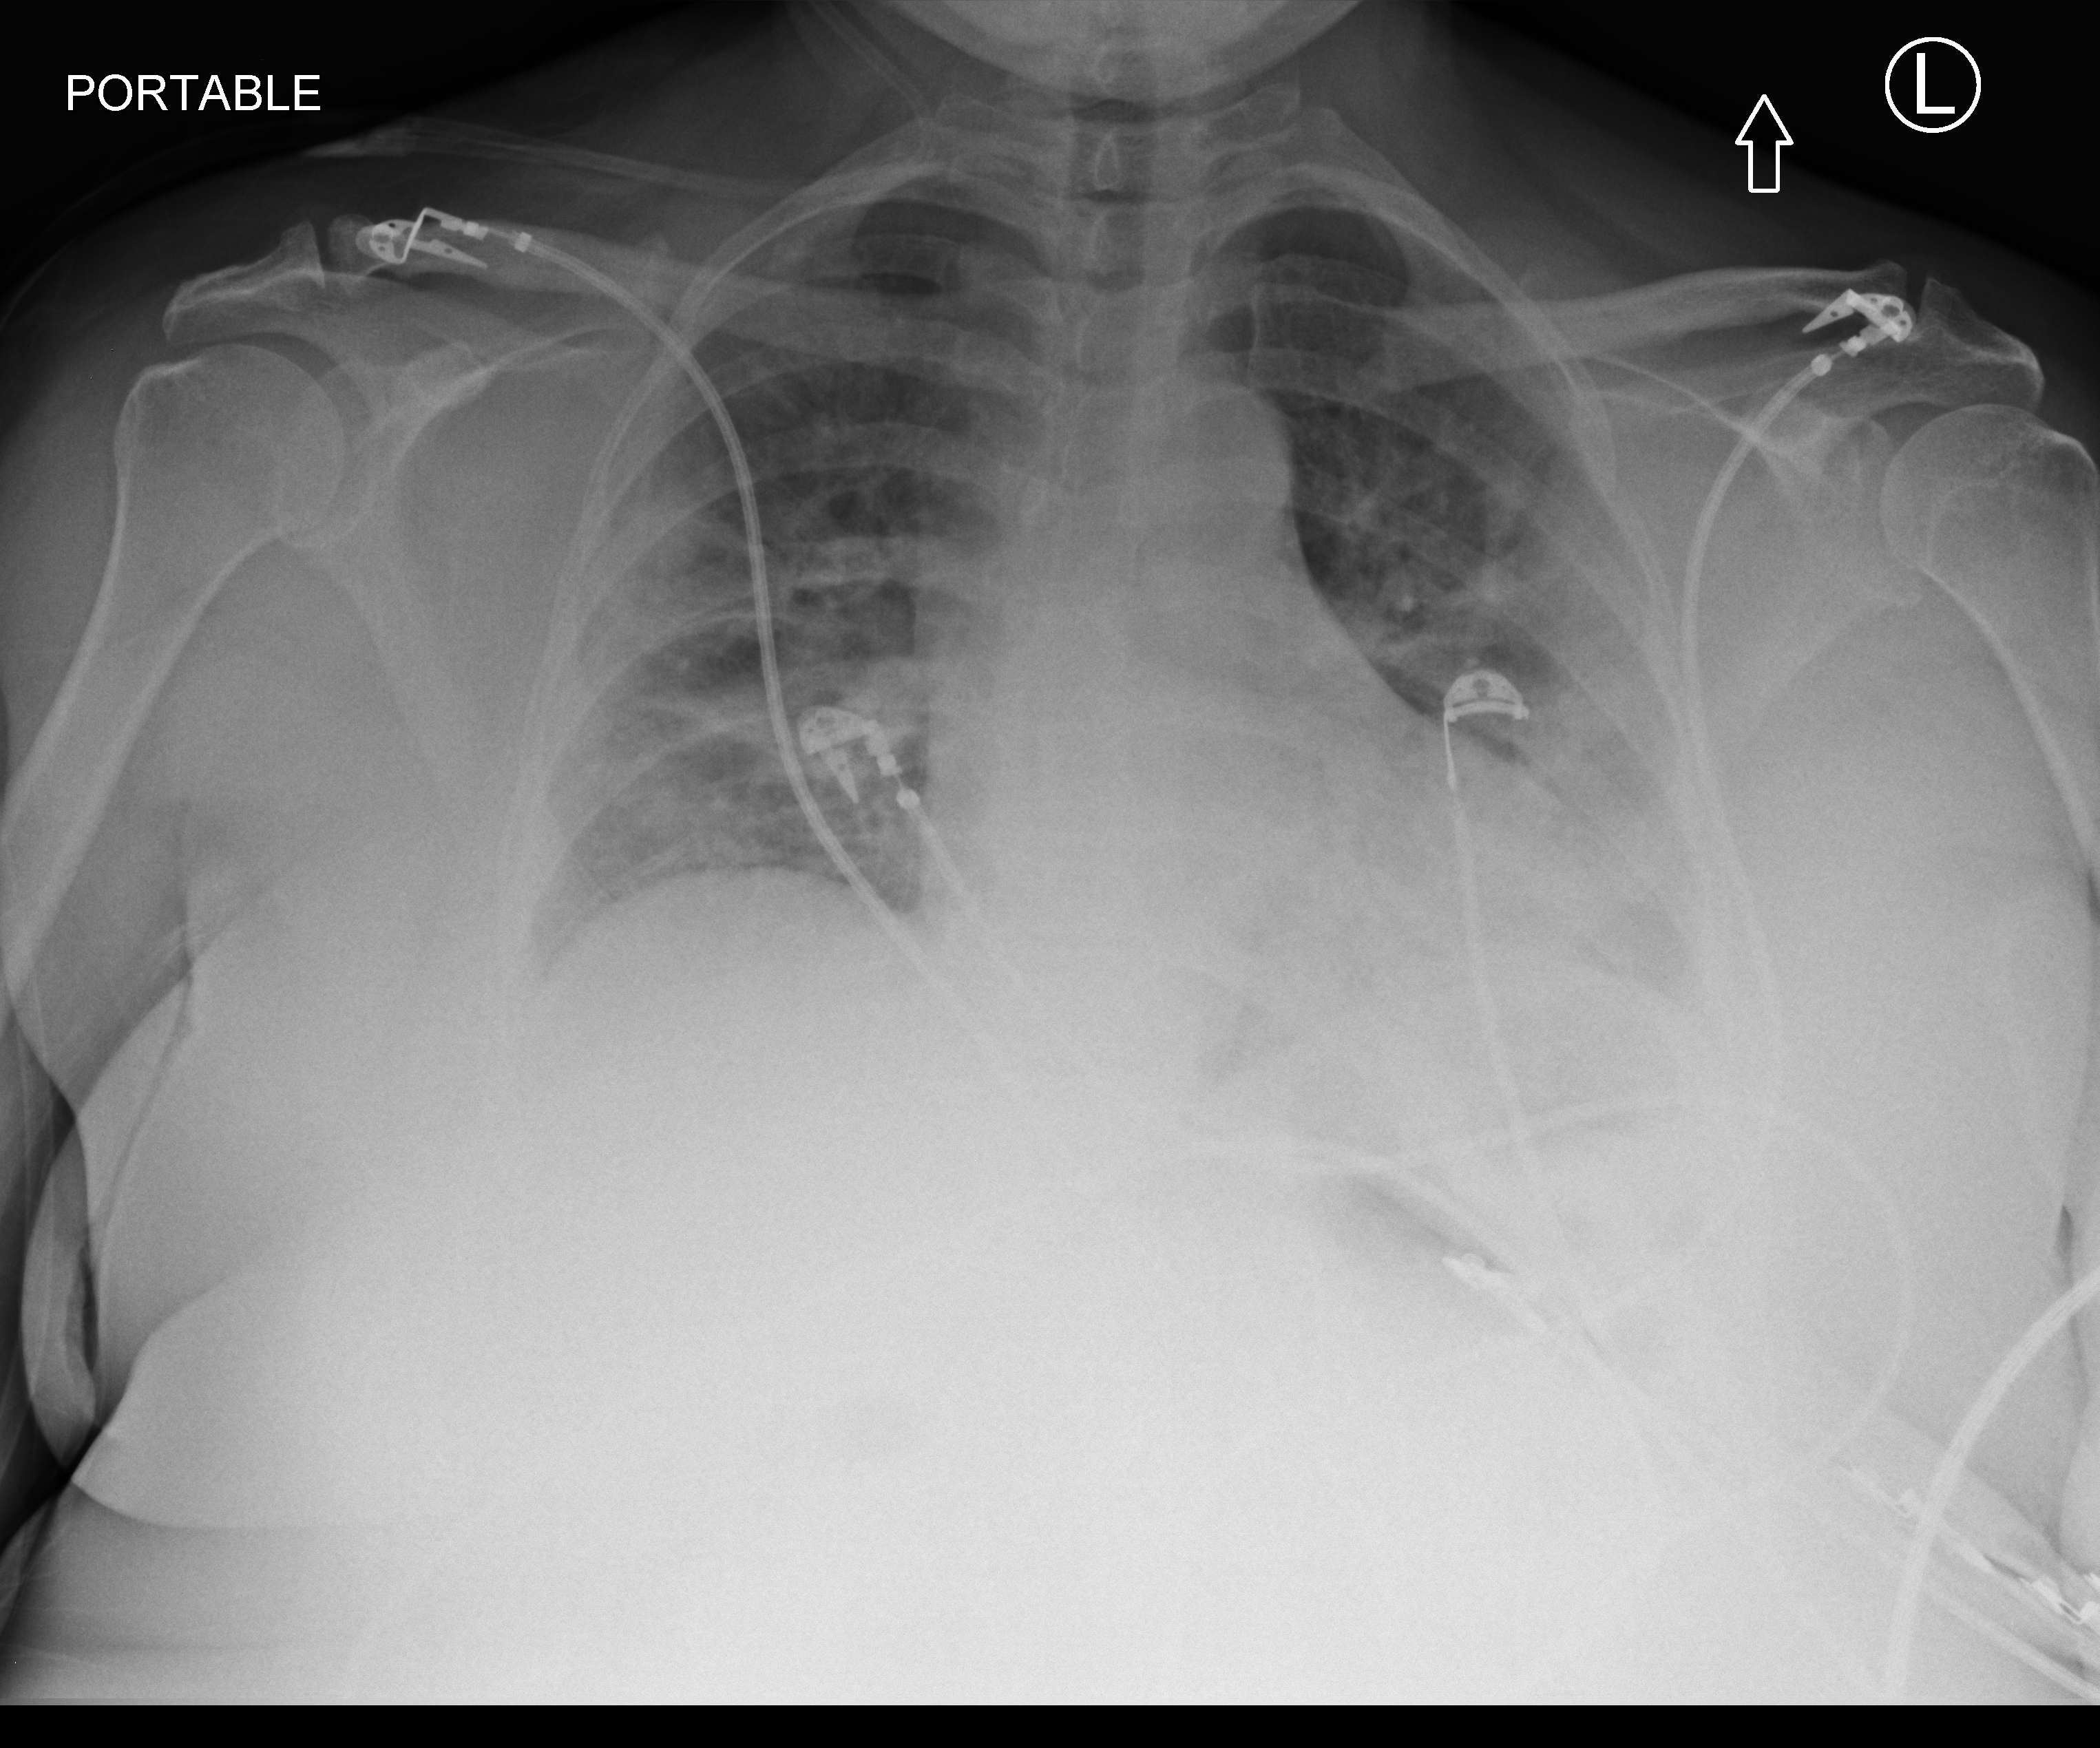
Chest X-ray (portable). Female patient hospitalised with COVID-19, age 18–59 years.
From the hospital-stay record, not from the radiograph (when in the stay this image was taken is not recorded): other chronic lung disease (admission record): no; diabetes (admission record): no.